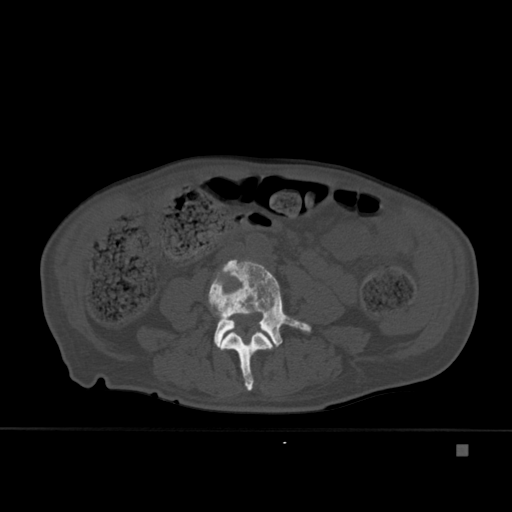
CT including the spine, one axial slice. Slice 131 of 451 in the series (ordered by position). Bone window (W 1800 / L 400 HU). 1.5 mm slice thickness. 512 × 512 image matrix. Male patient, age 75 years. From the clinical record (not read from this slice): primary cancer: prostate.
Structures marked on this image (semi-automatic segmentation, software-assisted and operator-edited):
- L3 vertebra: bounding box (x1, y1, x2, y2) in pixels: (219, 331, 274, 391)
- L4 vertebra: (208, 259, 311, 380)